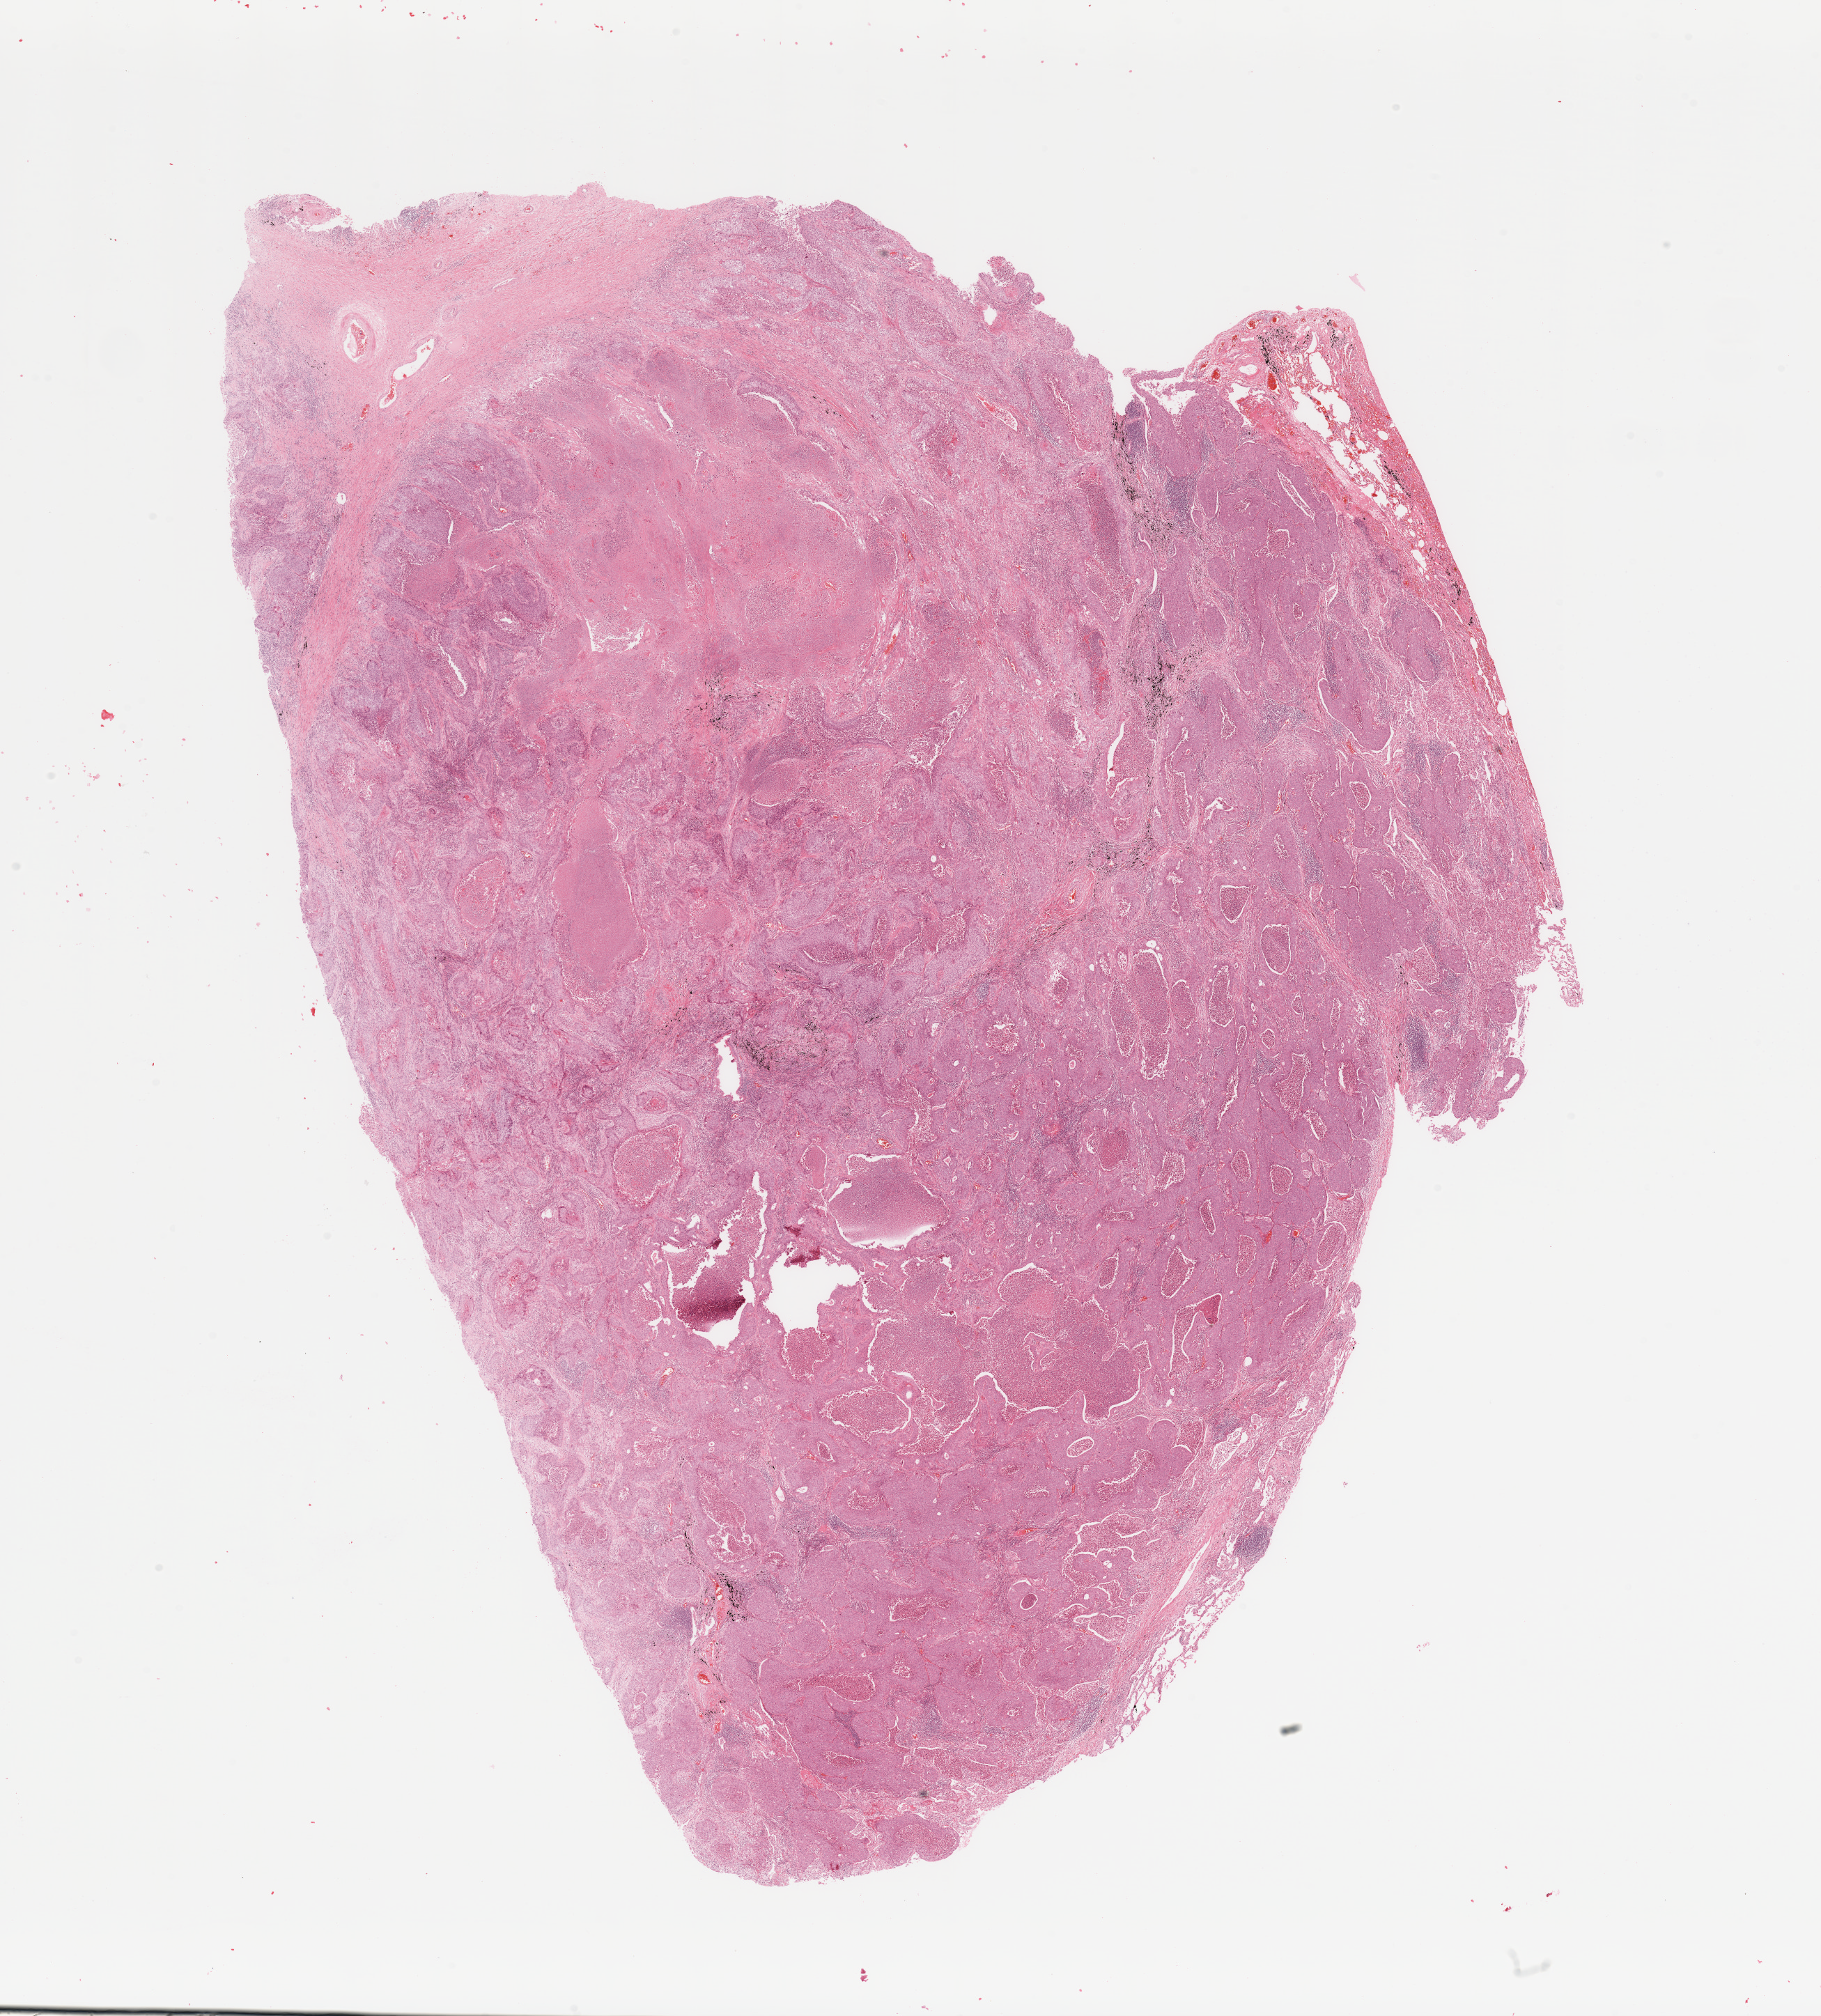
Hematoxylin and eosin (H&E) stained whole-slide image, a low-resolution overview of the entire scanned area, about 20.7 x 22.9 mm (from a 20x scan). Lung, tumour tissue. Male, 72 y/o. Histologic grade: G3 (poorly differentiated).
AJCC pathologic stage: IB. Histologic diagnosis: Squamous cell carcinoma, NOS.